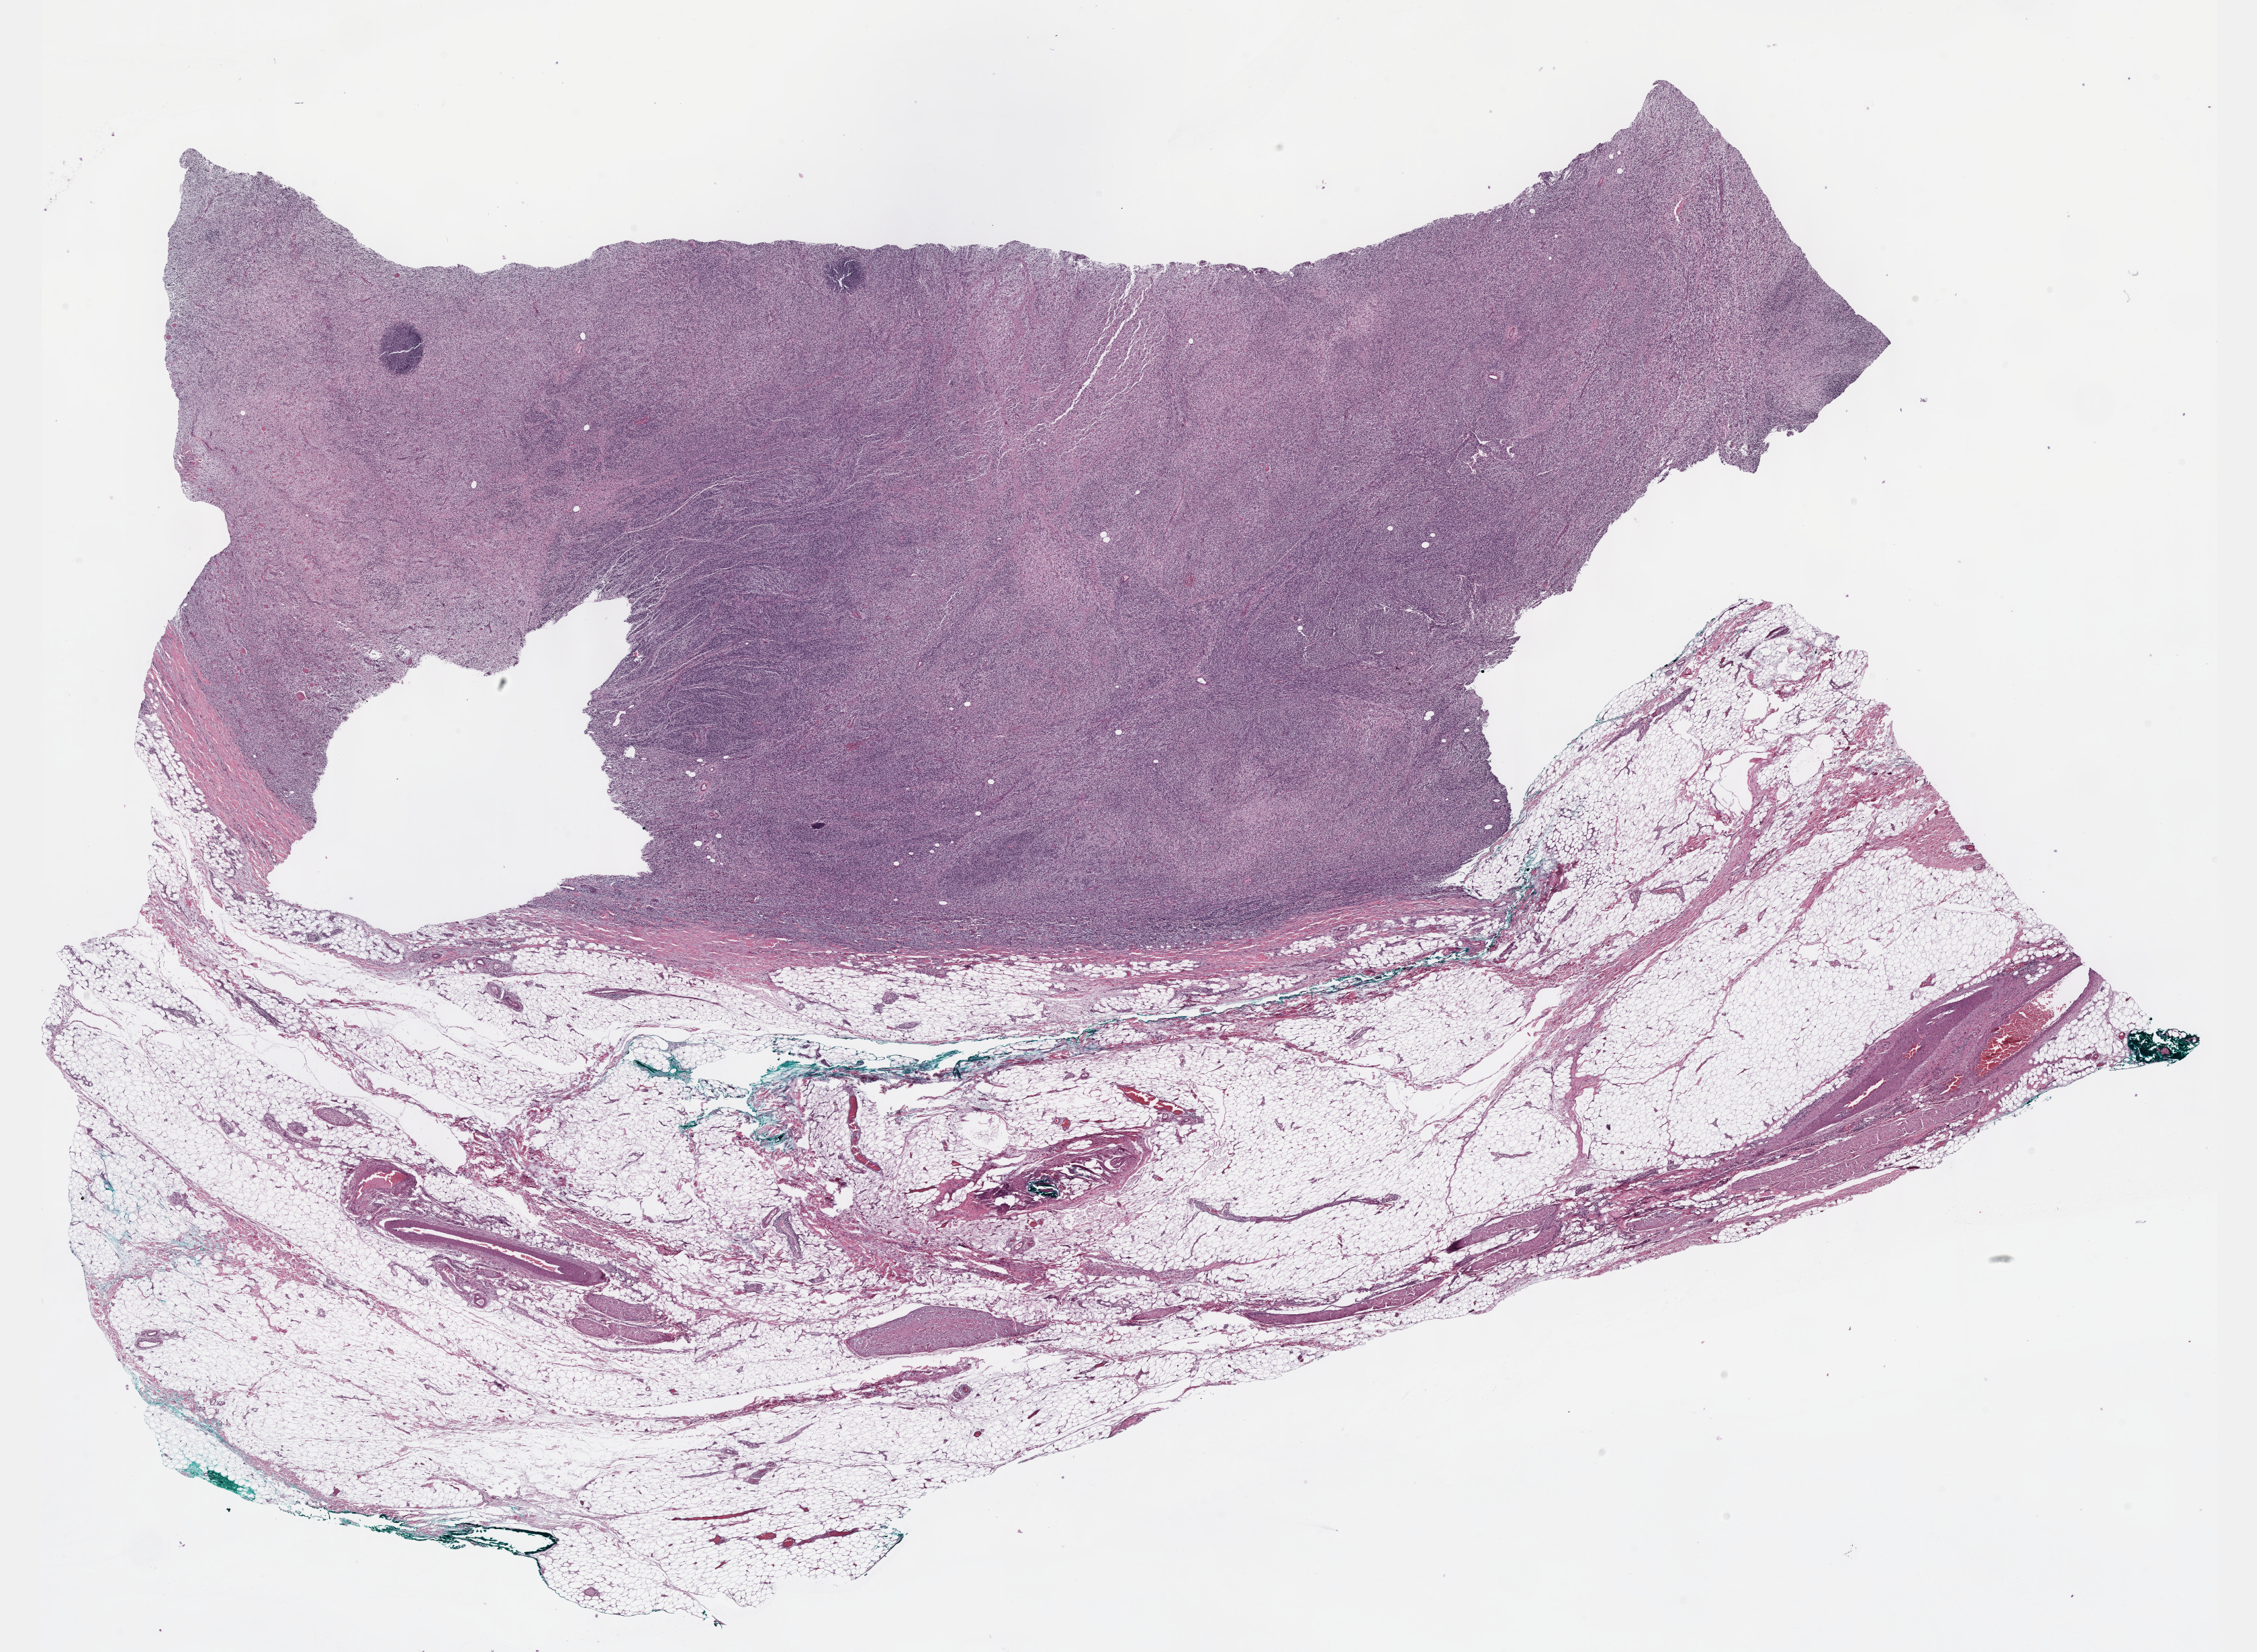
Whole-slide histology image, H&E — a low-resolution overview of the entire scanned area, about 27.2 x 19.9 mm; FFPE section; connective, subcutaneous and other soft tissues, primary tumour sample. Female patient; age at initial diagnosis 34 years.
• pathologic diagnosis: Malignant peripheral nerve sheath tumor (connective, subcutaneous and other soft tissues of thorax)